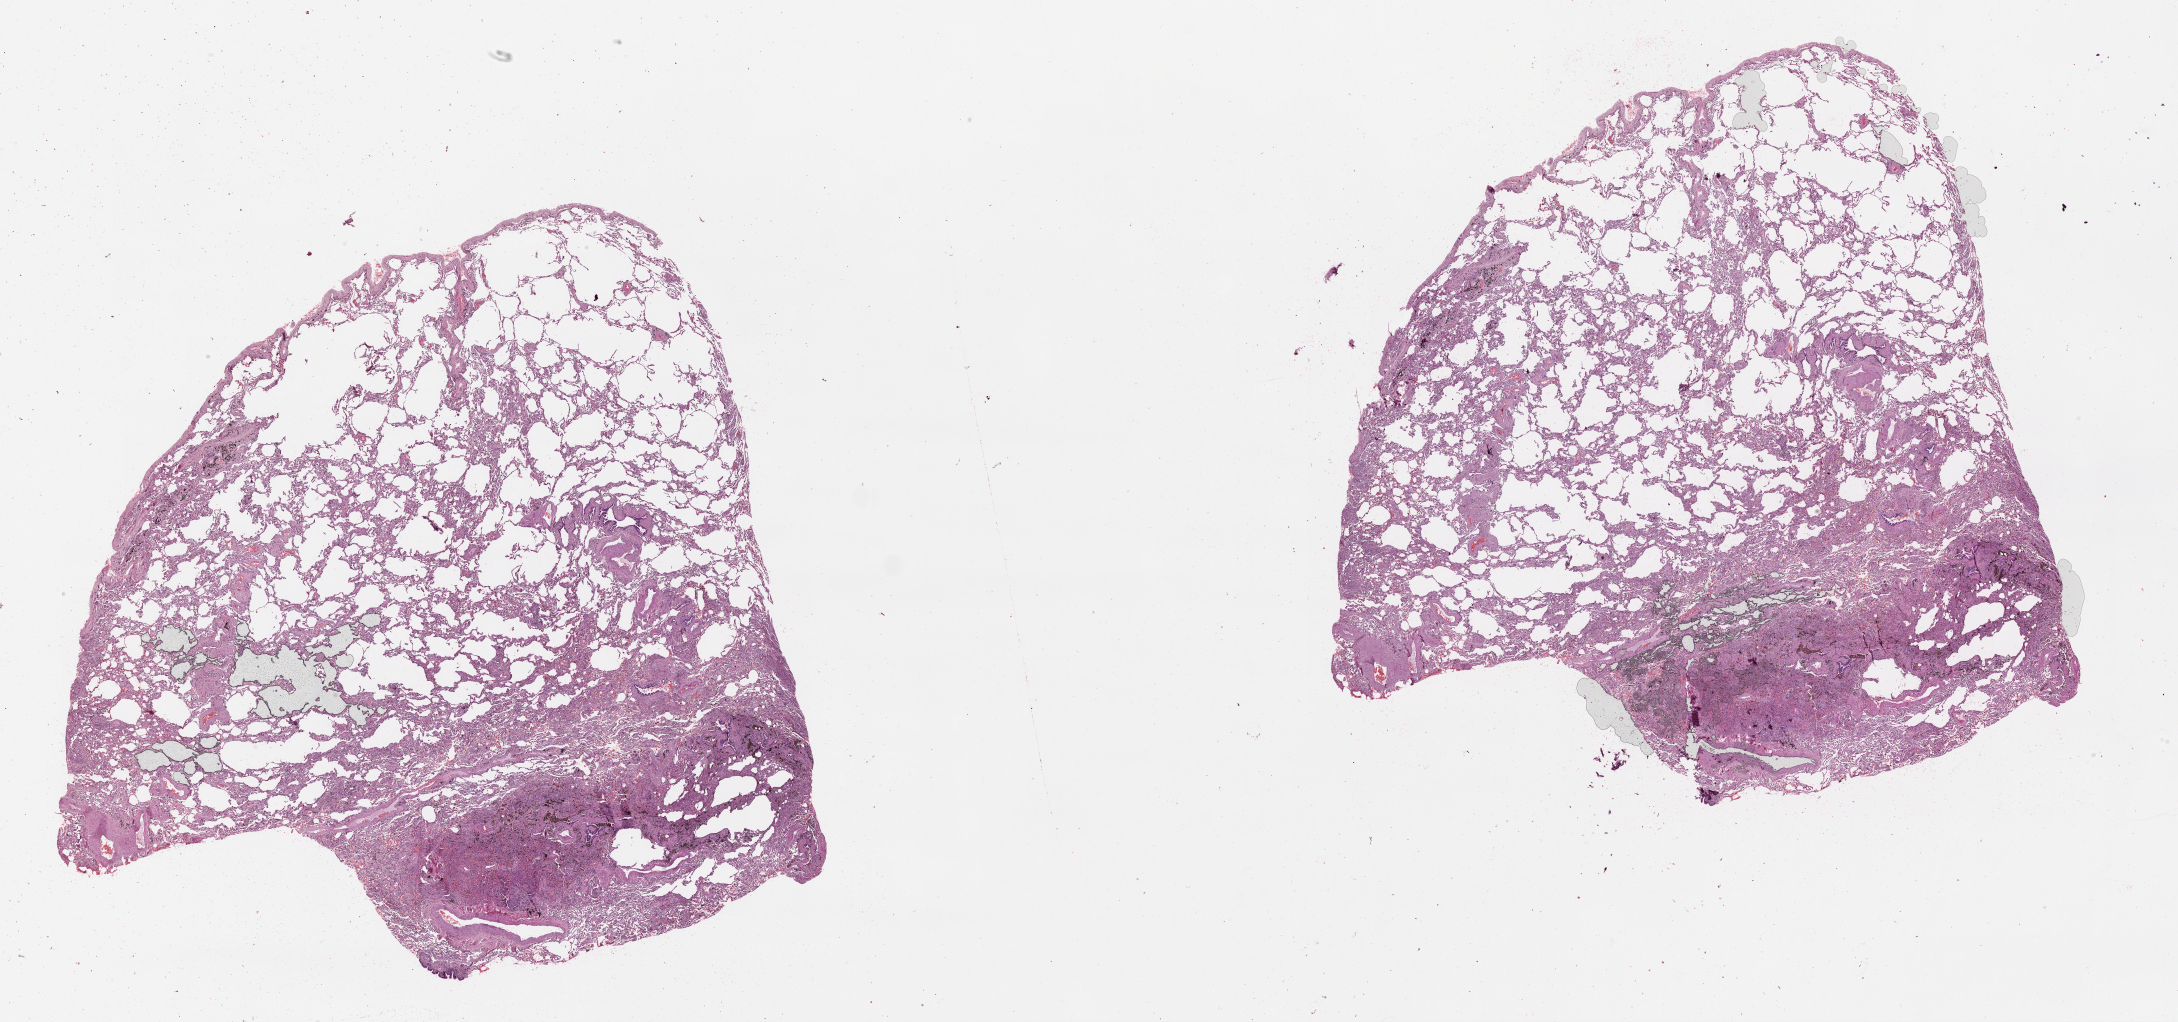
Whole-slide histology image, H&E-stained, whole scanned area (about 35.1 x 16.5 mm) shown as a low-resolution overview, normal (non-tumour) tissue sample, lung. Male, 59 y/o.
This section: normal (non-tumour) tissue from the same patient. Patient diagnosis (cohort enrolment): squamous cell carcinoma (lung).